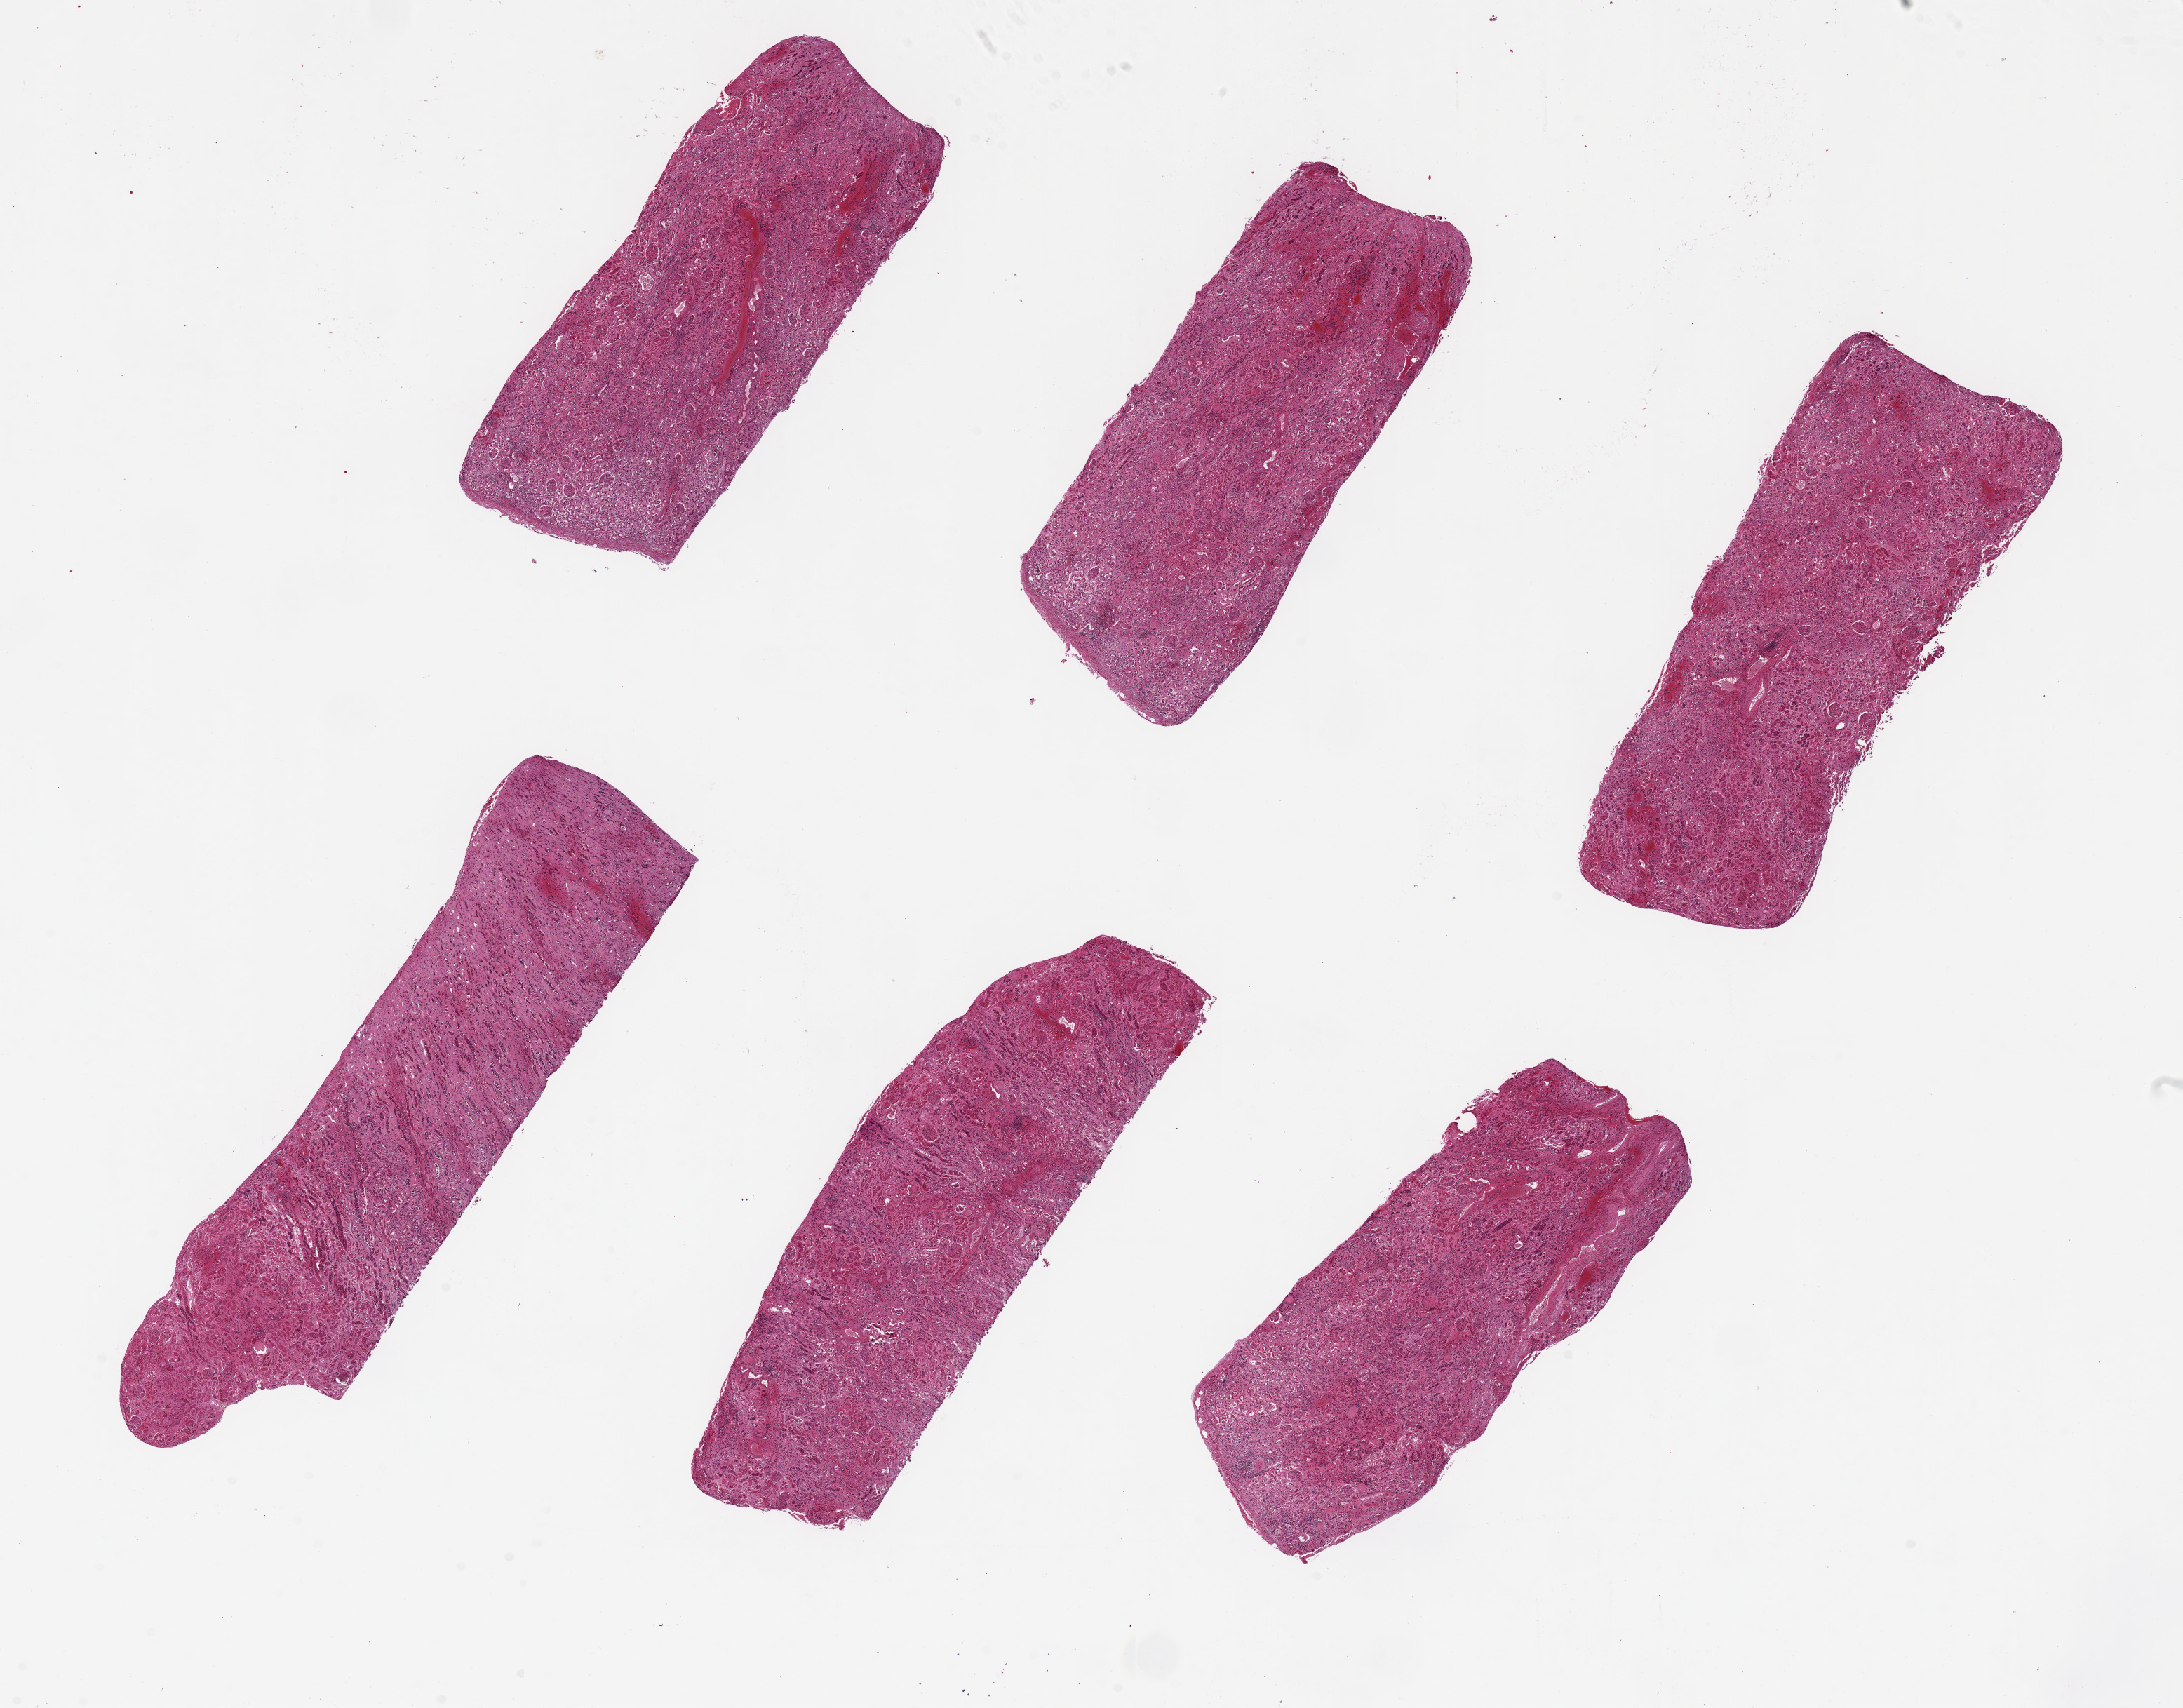
Whole-slide image, H&E stain — whole scanned area (about 24.6 x 19.3 mm, acquisition: 20x scan) shown as a low-resolution overview; PAXgene-fixed paraffin-embedded (PFPE) section; target tissue: renal cortex; tissue donor sample. Female donor.
Reviewer comment on this tissue sample: 6 pieces, up to 9x2mm; badly autolyzed.